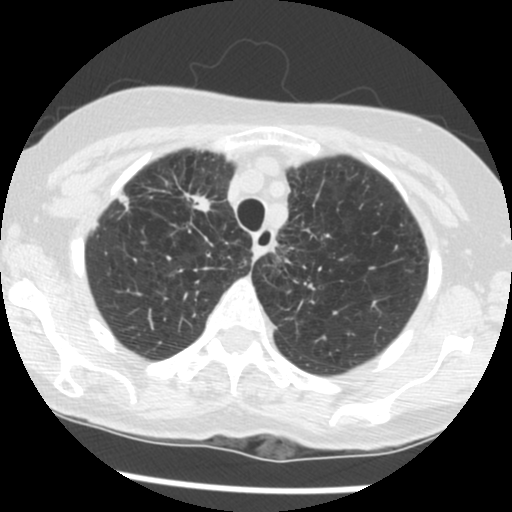
Low-dose screening chest CT, one axial slice; slice 101 of 124 in the series (ordered by position); reconstruction kernel STANDARD; 120 kVp; lung window (W 1500 / L -600 HU); 2.5 mm slice thickness; 512 × 512 image matrix, field of view 290 × 290 mm.
Outlined on this slice (manually delineated by an expert):
- lesion 1 (tumor, upper lobe of right lung): bounding box <185,193,211,212> (left, top, right, bottom; pixels)